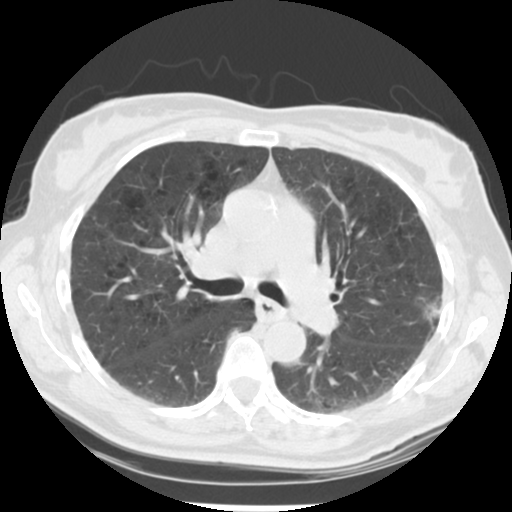
Low-dose screening chest CT, one axial slice; position 135 of 223 along the scan axis; reconstruction kernel STANDARD; lung window (W 1500 / L -600 HU); 512 × 512 image matrix.
Annotated regions visible in this slice (manually delineated by an expert):
- lesion 1 (tumor, upper lobe of left lung): bounding box <424,302,440,322> (left, top, right, bottom; pixels)